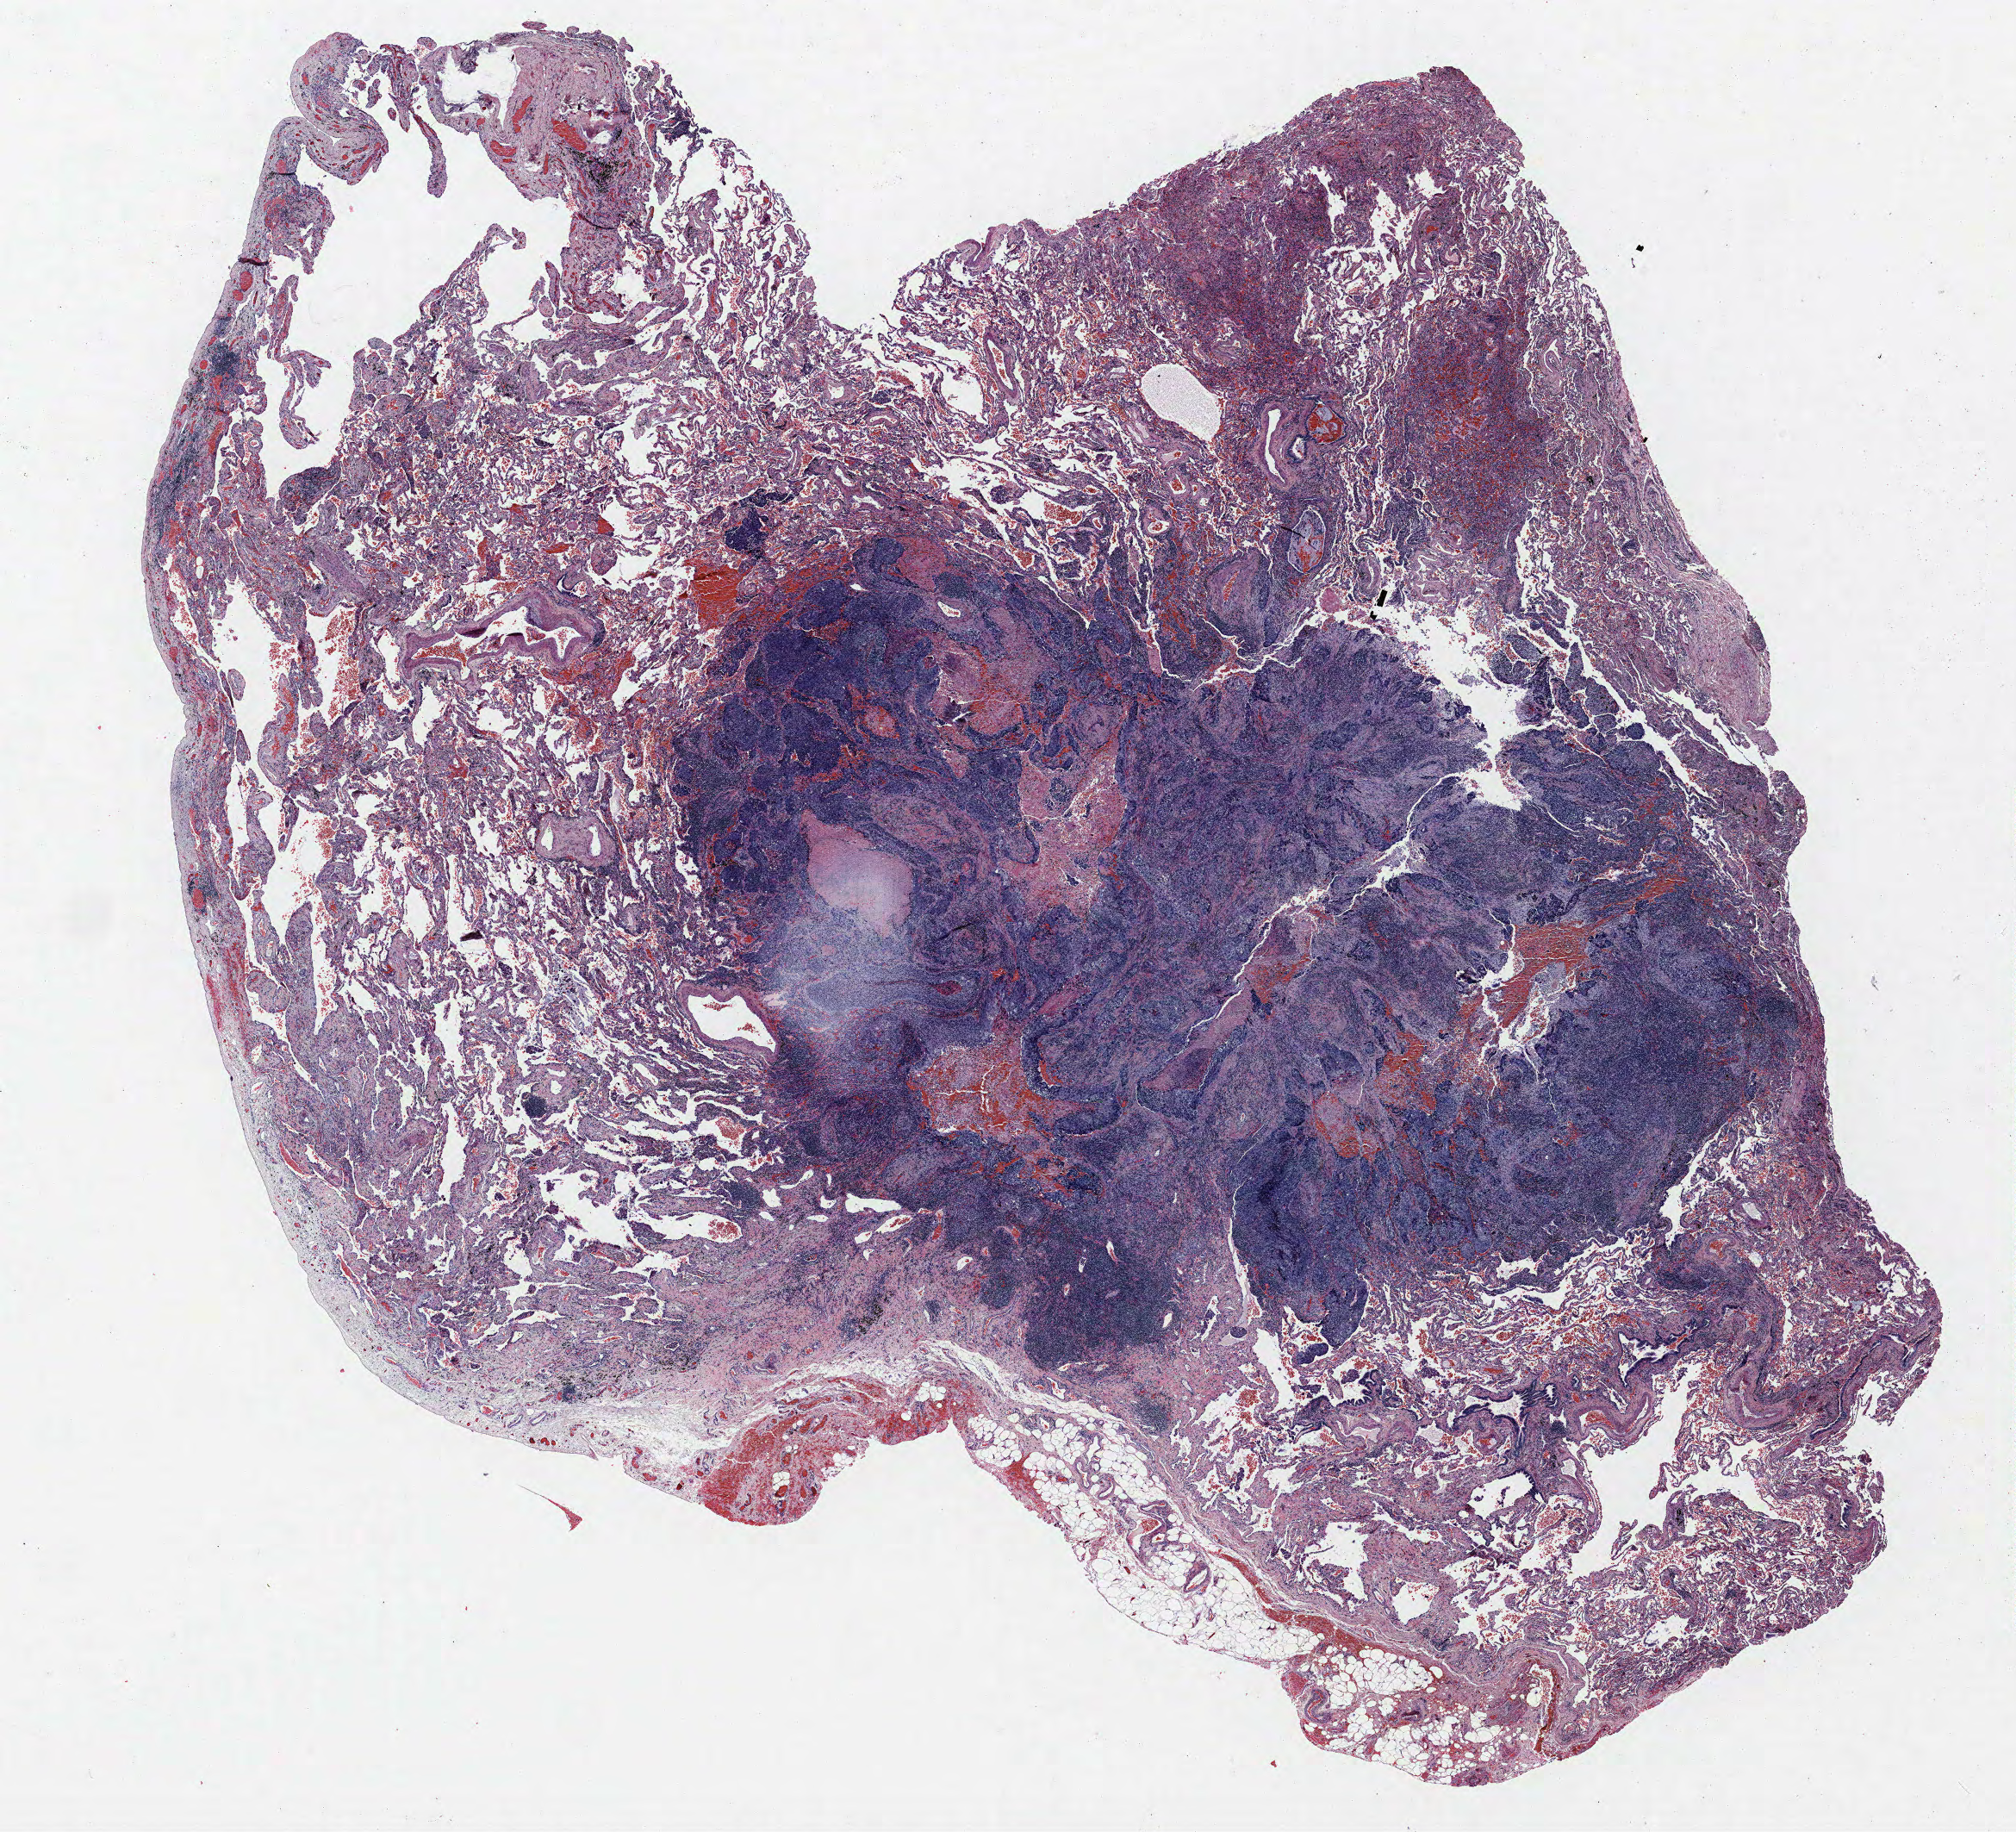
Whole-slide histology image, H&E-stained, low-resolution overview of the scanned area, about 18.7 x 17.0 mm (from a 40x scan); formalin-fixed paraffin-embedded (FFPE) section; lung. Male patient, aged 58 at enrolment. Former smoker at enrolment.
Participant's lung-cancer diagnosis: Squamous cell carcinoma, NOS (ICD-O-3 8070/3).